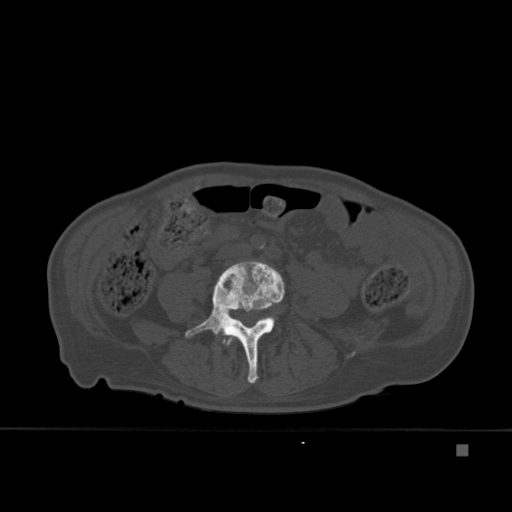
CT including the spine, one axial slice. Slice 122 of 451 in the series (ordered by position). Bone window (W 1800 / L 400 HU). 1.5 mm slice thickness. 512 × 512 image matrix. Patient: male, 75 years. Case-level facts recorded for this patient, not image findings: primary cancer: prostate.
Annotated regions visible in this slice (semi-automatically segmented with operator editing):
- L3 vertebra: bounding box <226,339,232,346> (left, top, right, bottom; pixels)
- L4 vertebra: <185,261,285,383>